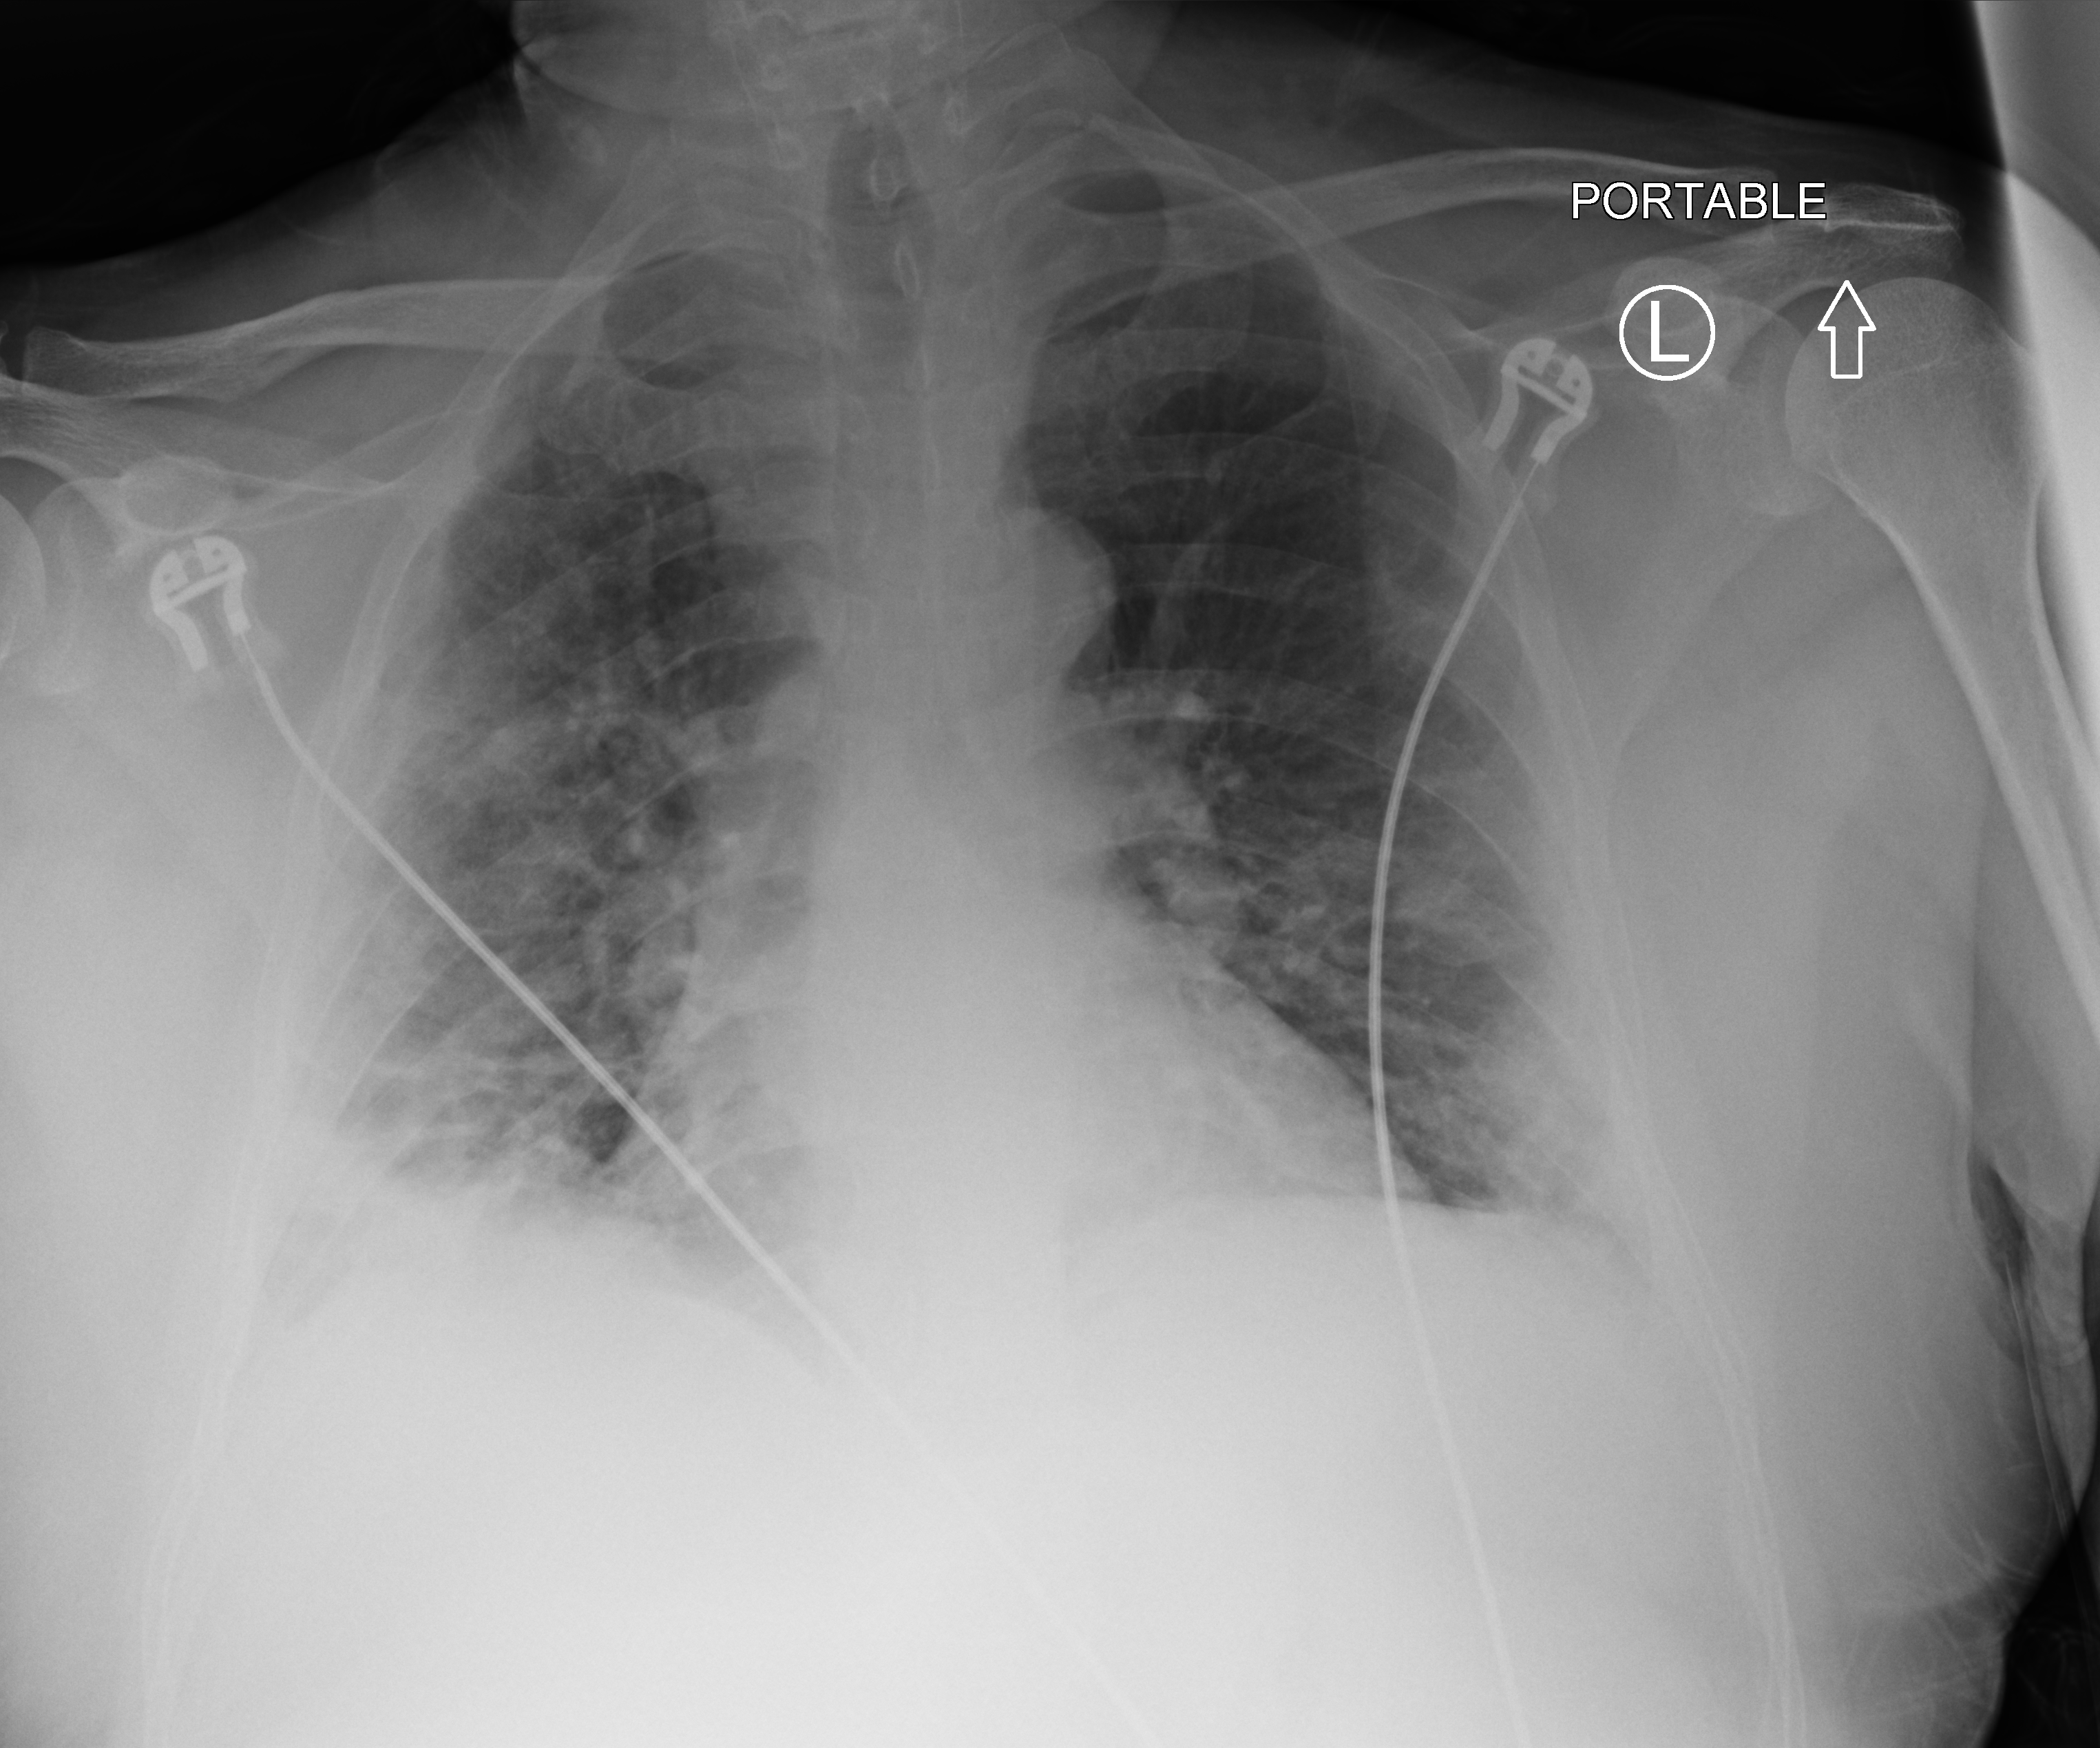
Bedside chest radiograph (computed radiography), anteroposterior (AP) projection. Patient hospitalised with COVID-19; male, aged 60–74 years.
Admission-level facts for this patient (not findings on this image; timing relative to this image not recorded): other chronic lung disease (admission record): no; length of hospital stay: 5 days; COPD (admission record): no.